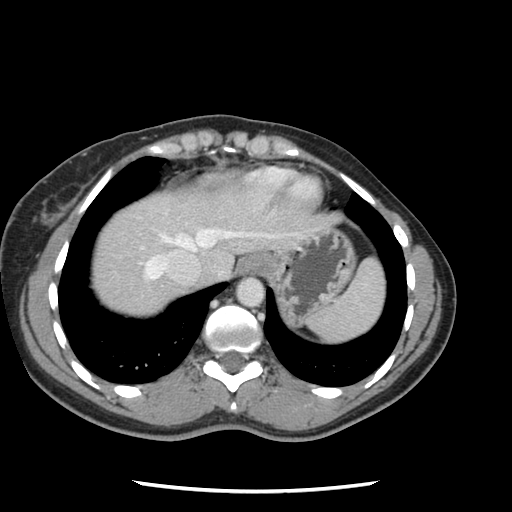
Contrast-enhanced abdominal CT, one axial slice. Position 107 of 134 along the scan axis. 120 kVp. Intravenous contrast given. Soft-tissue window (W 400 / L 40 HU). 2.5 mm slice thickness. 512 × 512 image matrix. Female patient, age 43 years. Case-level facts recorded for this patient, not image findings: diagnosis: colorectal cancer liver metastases, imaged before liver resection; multiple liver metastases: yes; largest metastasis: 3.4 cm; chemotherapy before resection: no.
Structures marked on this image (outlined manually by an expert reader):
- hepatic veins: bounding box <145,229,270,280> (left, top, right, bottom; pixels)
- liver: <91,195,298,316>
- planned liver remnant (the part of the liver to remain after resection): <92,195,203,299>
- portal vein (with intrahepatic branches): <140,246,143,249>